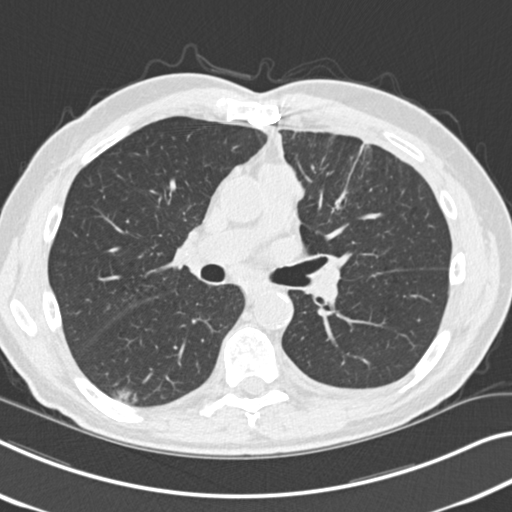
Chest CT (low-dose screening protocol), one axial image; baseline screening round; lung window (W 1500 / L -600 HU); standard (soft-tissue) reconstruction kernel (B30f); slice 100 of 212 in the series; 512 × 512 image matrix, field of view 338 × 338 mm. Male, age 68 years at enrolment.
- Expert-annotated lung lesion, box from (x=97, y=379) to (x=147, y=415) px.
- Reader record for this screening exam (exam-level; its link to the box is not recorded): non-calcified nodule or mass ≥4 mm, right lower lobe, 14 × 10 mm, poorly defined margins, ground glass attenuation.
- Official screen result: positive, change unspecified: nodule(s) >= 4 mm or enlarging nodule(s), mass(es), or other non-specific abnormalities suspicious for lung cancer.
- Participant outcome: lung cancer diagnosed 1018 days after this screen — non-small cell carcinoma, right lower lobe, poorly differentiated (G3), stage IA (AJCC 6th edition), 23 mm at pathology.